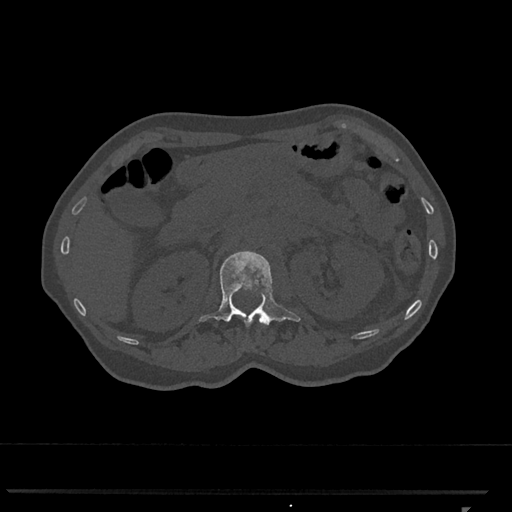
CT including the spine, one axial slice. Position 408 of 793 along the scan axis. Reconstruction kernel Br40s/3. Bone window (W 1800 / L 400 HU). 512 × 512 image matrix. Female patient, age 62 years. Case-level facts recorded for this patient, not image findings: primary cancer: renal.
Outlined on this slice (semi-automatically segmented with operator editing):
- L1 vertebra: bounding box [x1, y1, x2, y2] px = [199, 251, 301, 327]